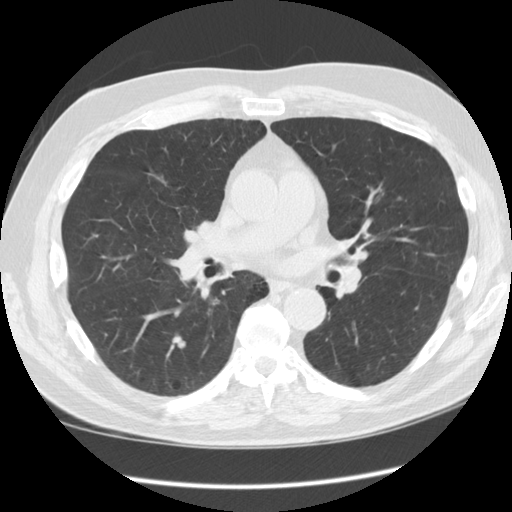
Low-dose screening chest CT, axial slice; third annual screen; lung window (W 1500 / L -600 HU); 2.5 mm slice thickness; 120 kVp. Male participant, aged 60 years at enrolment. Former smoker at enrolment.
• Lesion marked by an expert reader, box from (x=153, y=327) to (x=194, y=361) px.
• The screening reader recorded 5 non-calcified nodules or masses ≥4 mm on this exam (right middle lobe, right upper lobe, left upper lobe, left lower lobe, right upper lobe); which of them this box marks is not recorded.
• Lung cancer was diagnosed 353 days after this screen: squamous cell carcinoma, clear cell type, right lower lobe, stage IV (AJCC 6th edition), 12 mm at pathology.